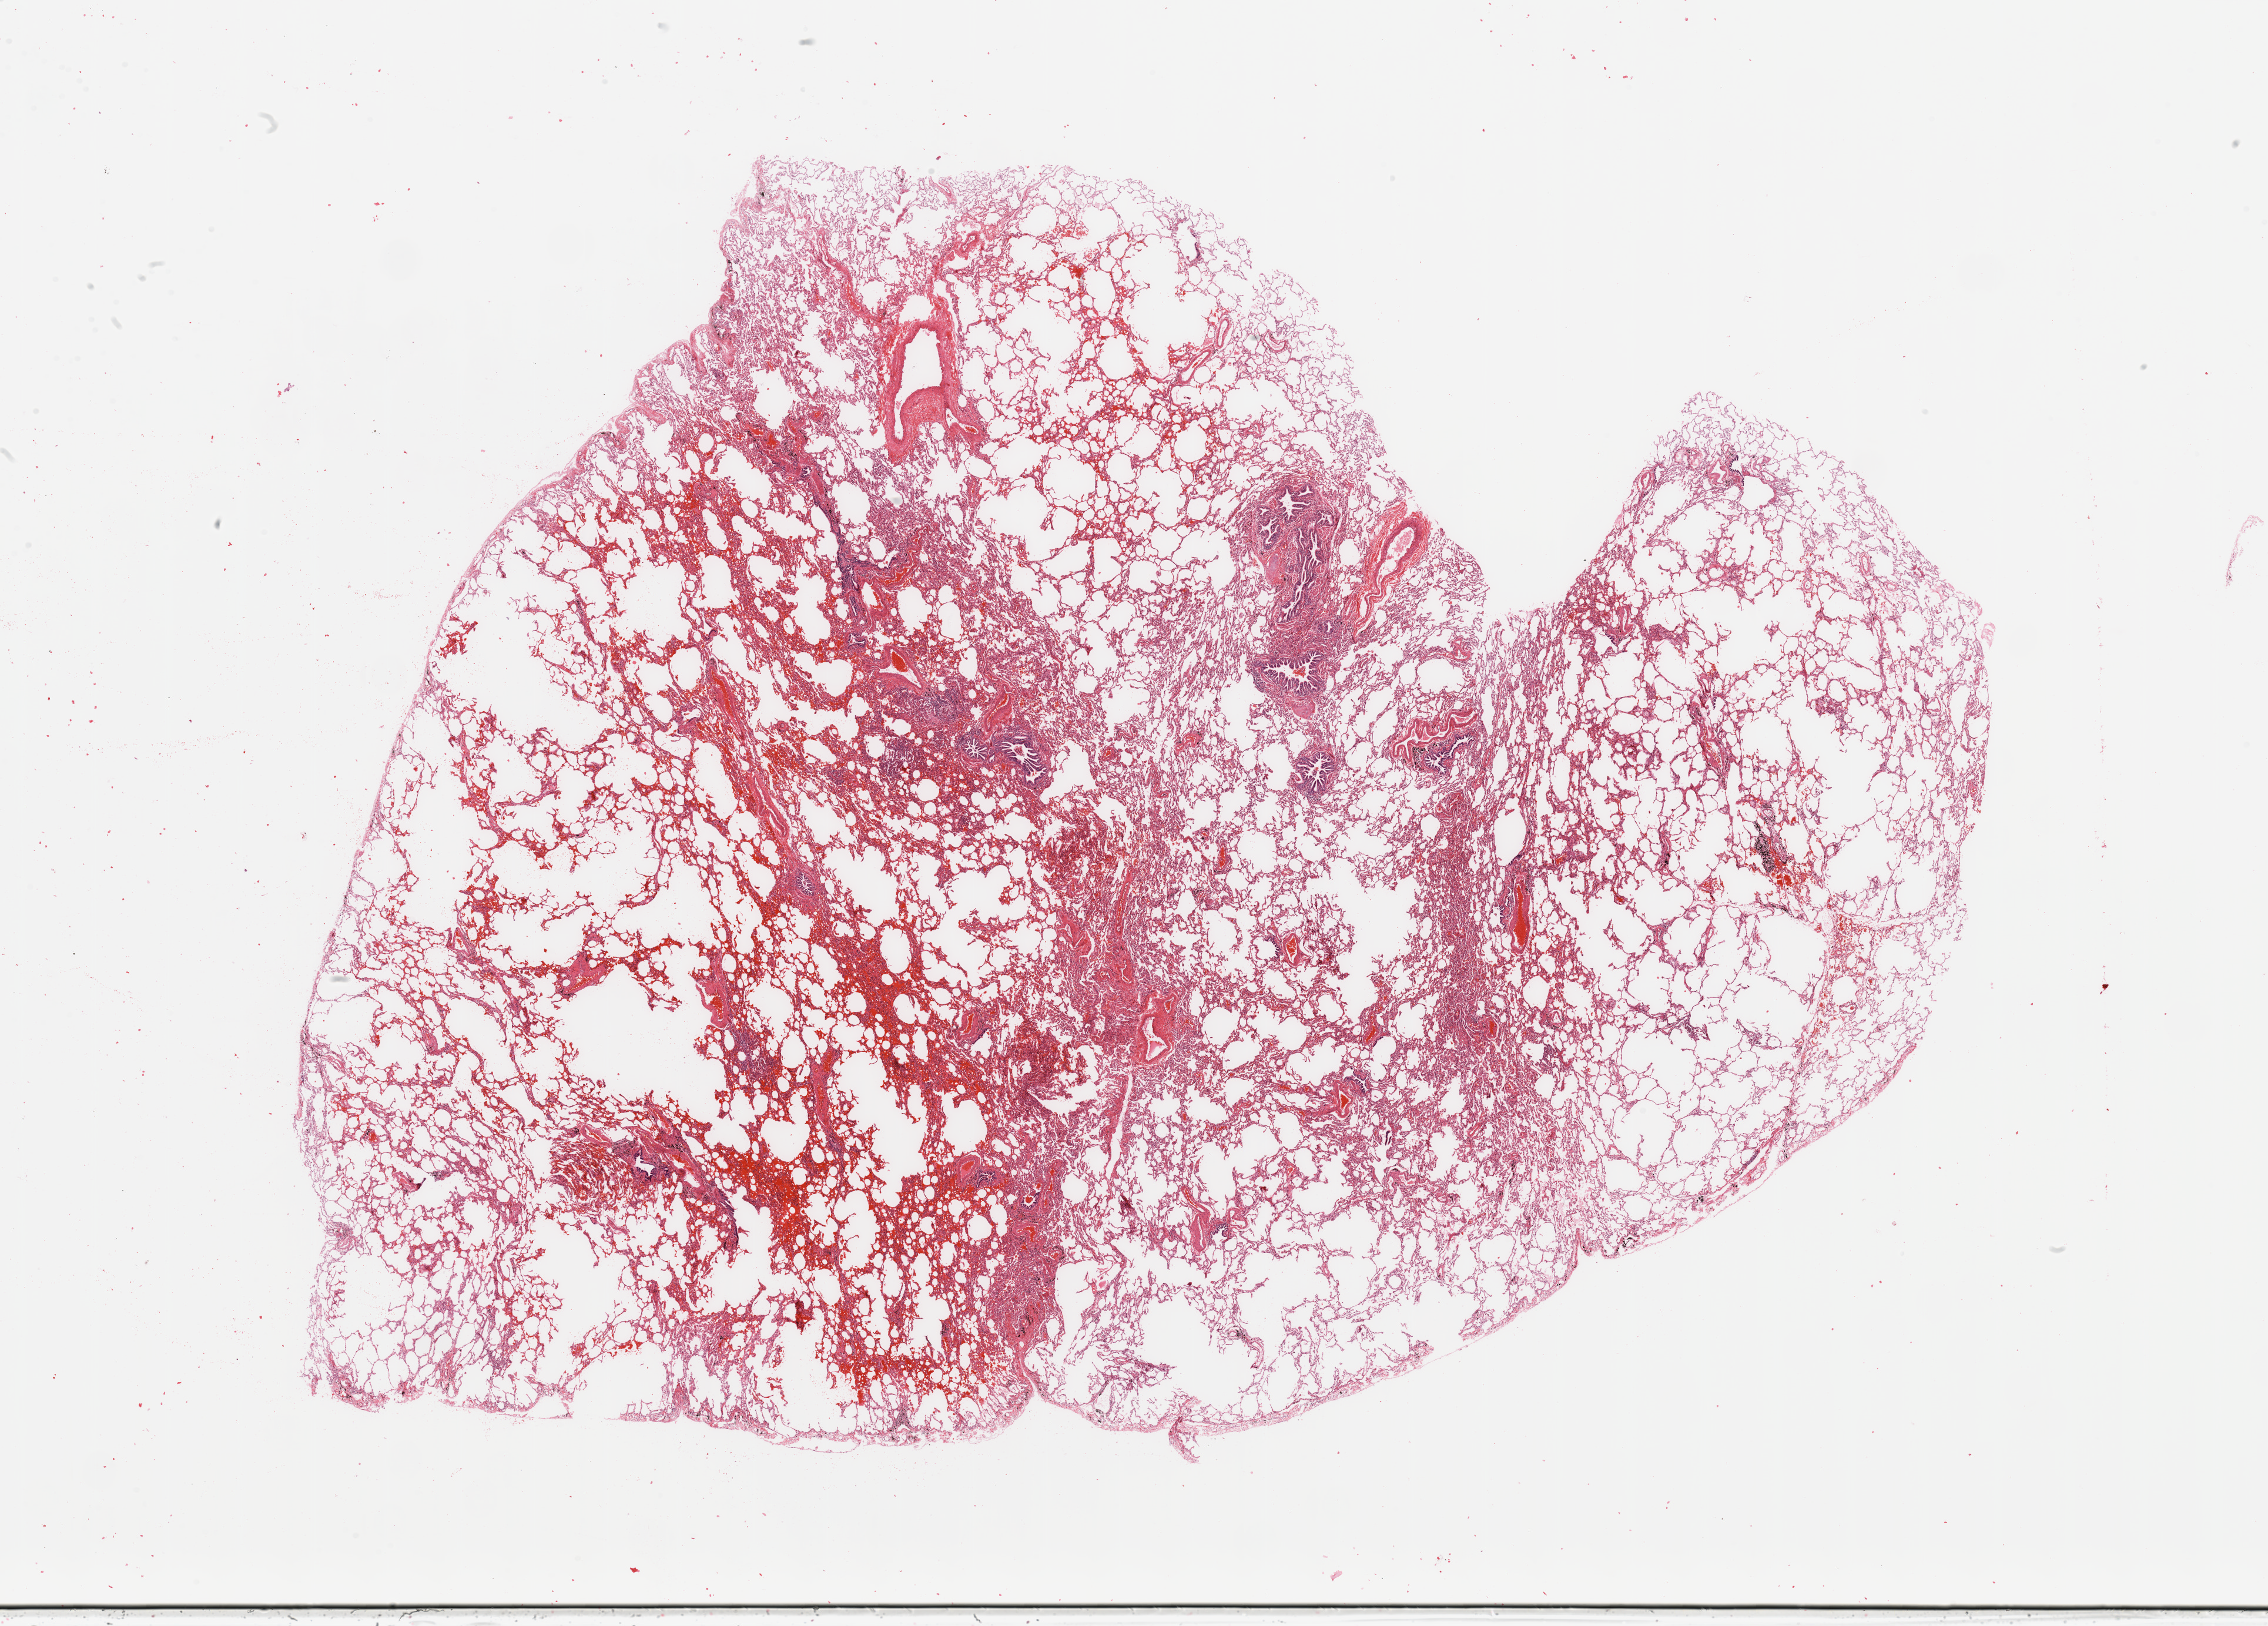
Digitized Hematoxylin and eosin (H&E) stained tissue section (whole slide), whole scanned area (about 30.5 x 21.9 mm, slide scanned at 20x) shown as a low-resolution overview. Lung, normal (non-tumour) tissue. Patient: male, age 55 years.
This section: normal (non-tumour) tissue from the same patient. Patient diagnosis: Adenocarcinoma, NOS.